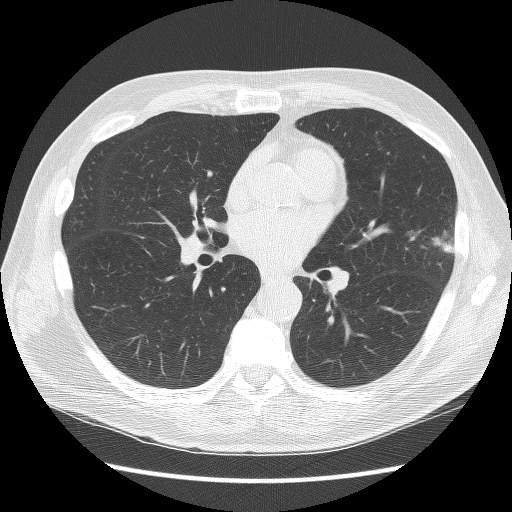
Chest CT (low-dose screening protocol), one axial image; third screening round (two years after baseline); lung window (W 1500 / L -600 HU); 2.5 mm slice thickness; 120 kVp; slice 63 of 134 in the series; 512 × 512 image matrix. Male participant, aged 67 years at enrolment. Former smoker at enrolment.
- Expert-annotated lung lesion, bounding box [x1, y1, x2, y2] px = [406, 211, 475, 283].
- Screening reader's record for this exam (one nodule recorded; not confirmed to be the boxed lesion): non-calcified nodule or mass ≥4 mm, left upper lobe, 22 × 17 mm, poorly defined margins, soft tissue attenuation, pre-existing on the prior screen: yes; interval growth: yes.
- Participant outcome: lung cancer diagnosed 72 days after this screen — squamous cell carcinoma, NOS, left upper lobe, moderately differentiated (G2), stage IB (AJCC 6th edition), 25 mm at pathology.